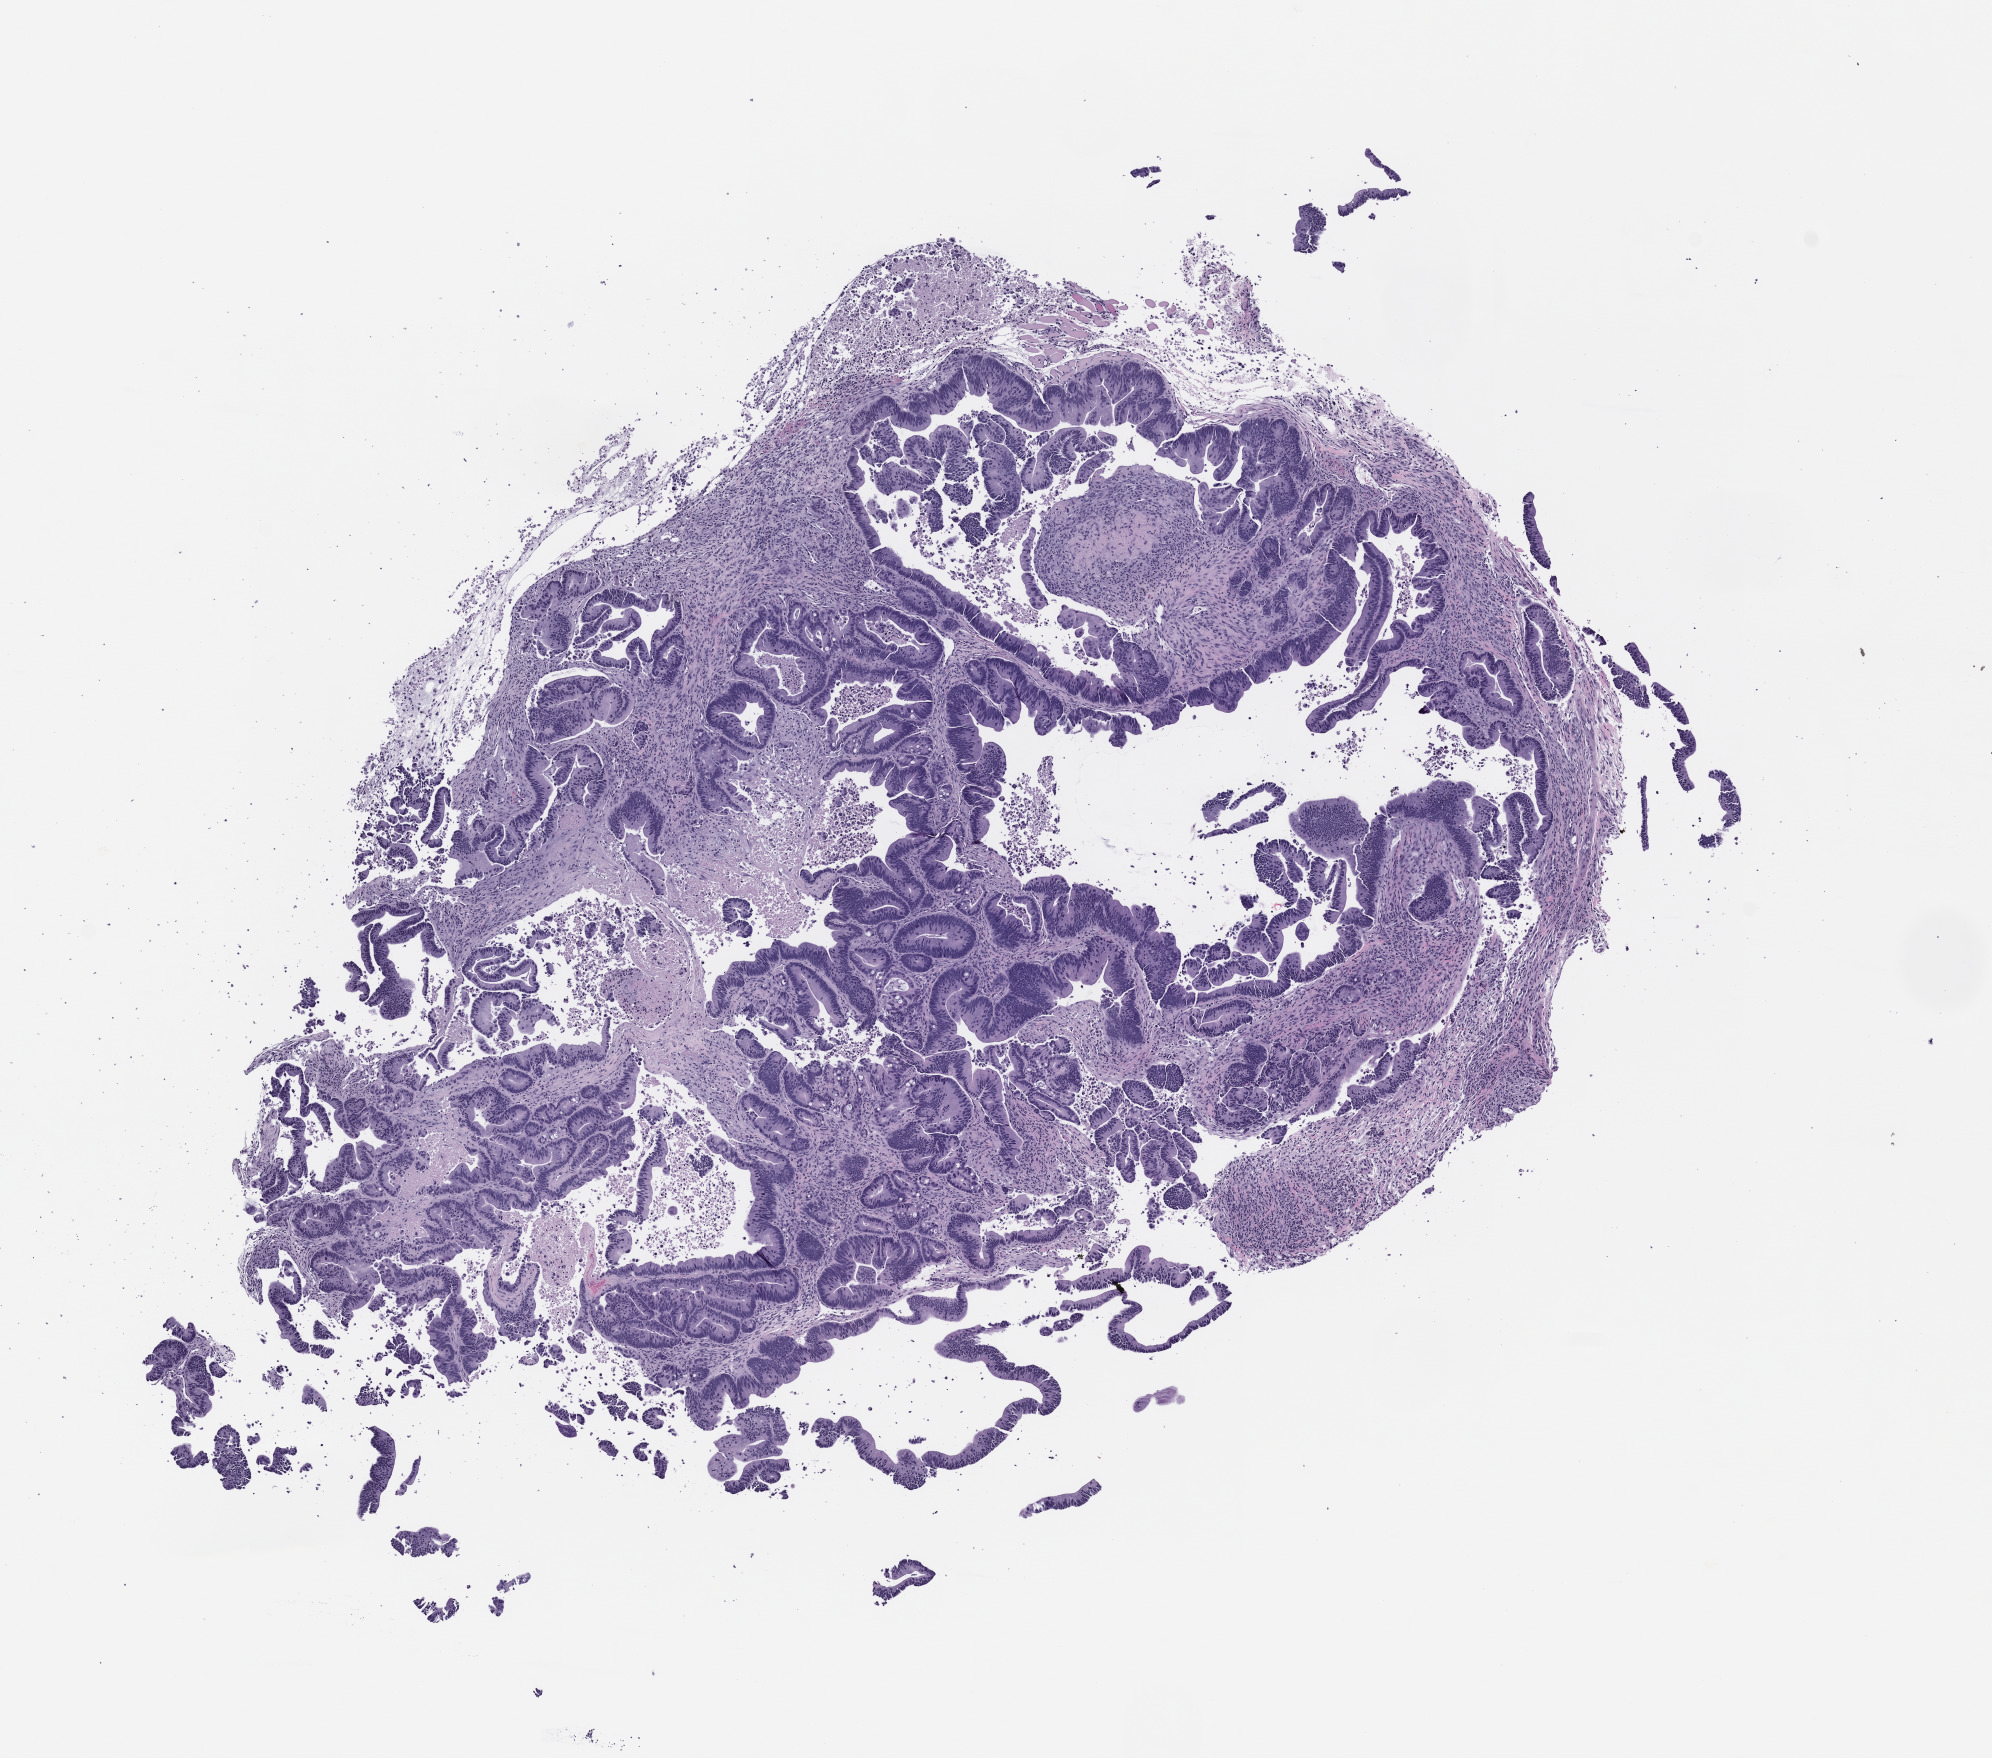
H&E whole-slide image of a patient-derived xenograft (PDX) tumor grown in a mouse, passage 4, low-resolution overview of the scanned area, about 8.0 x 7.1 mm, FFPE section, tumor site category: gastrointestinal tract.
• originating patient diagnosis: Colorectal Carcinoma